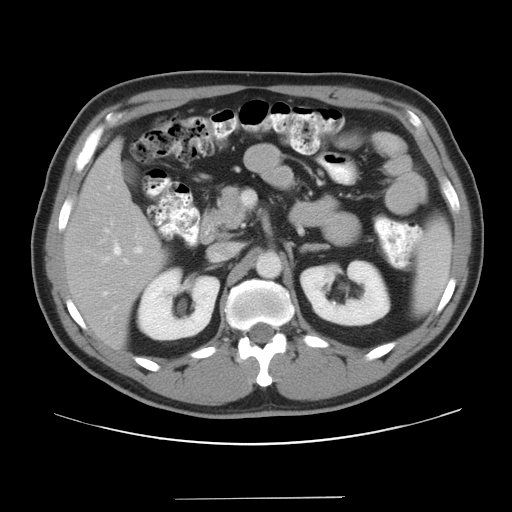
Contrast-enhanced abdominal CT, one axial slice; slice 20 of 37 in the series (ordered by position); 120 kVp; intravenous contrast given; soft-tissue window (W 400 / L 40 HU); 512 × 512 image matrix. Male patient, age 46 years. From the clinical record (not read from this slice): diagnosis: colorectal cancer liver metastases, imaged before liver resection; multiple liver metastases: yes; largest metastasis: 1 cm; disease in both lobes: no.
Structures marked on this image (outlined manually by an expert reader):
- hepatic veins: bounding box (x1, y1, x2, y2) in pixels: (103, 243, 128, 295)
- liver: (65, 146, 162, 346)
- planned liver remnant (the part of the liver to remain after resection): (65, 147, 162, 346)
- portal vein (with intrahepatic branches): (135, 246, 142, 253)